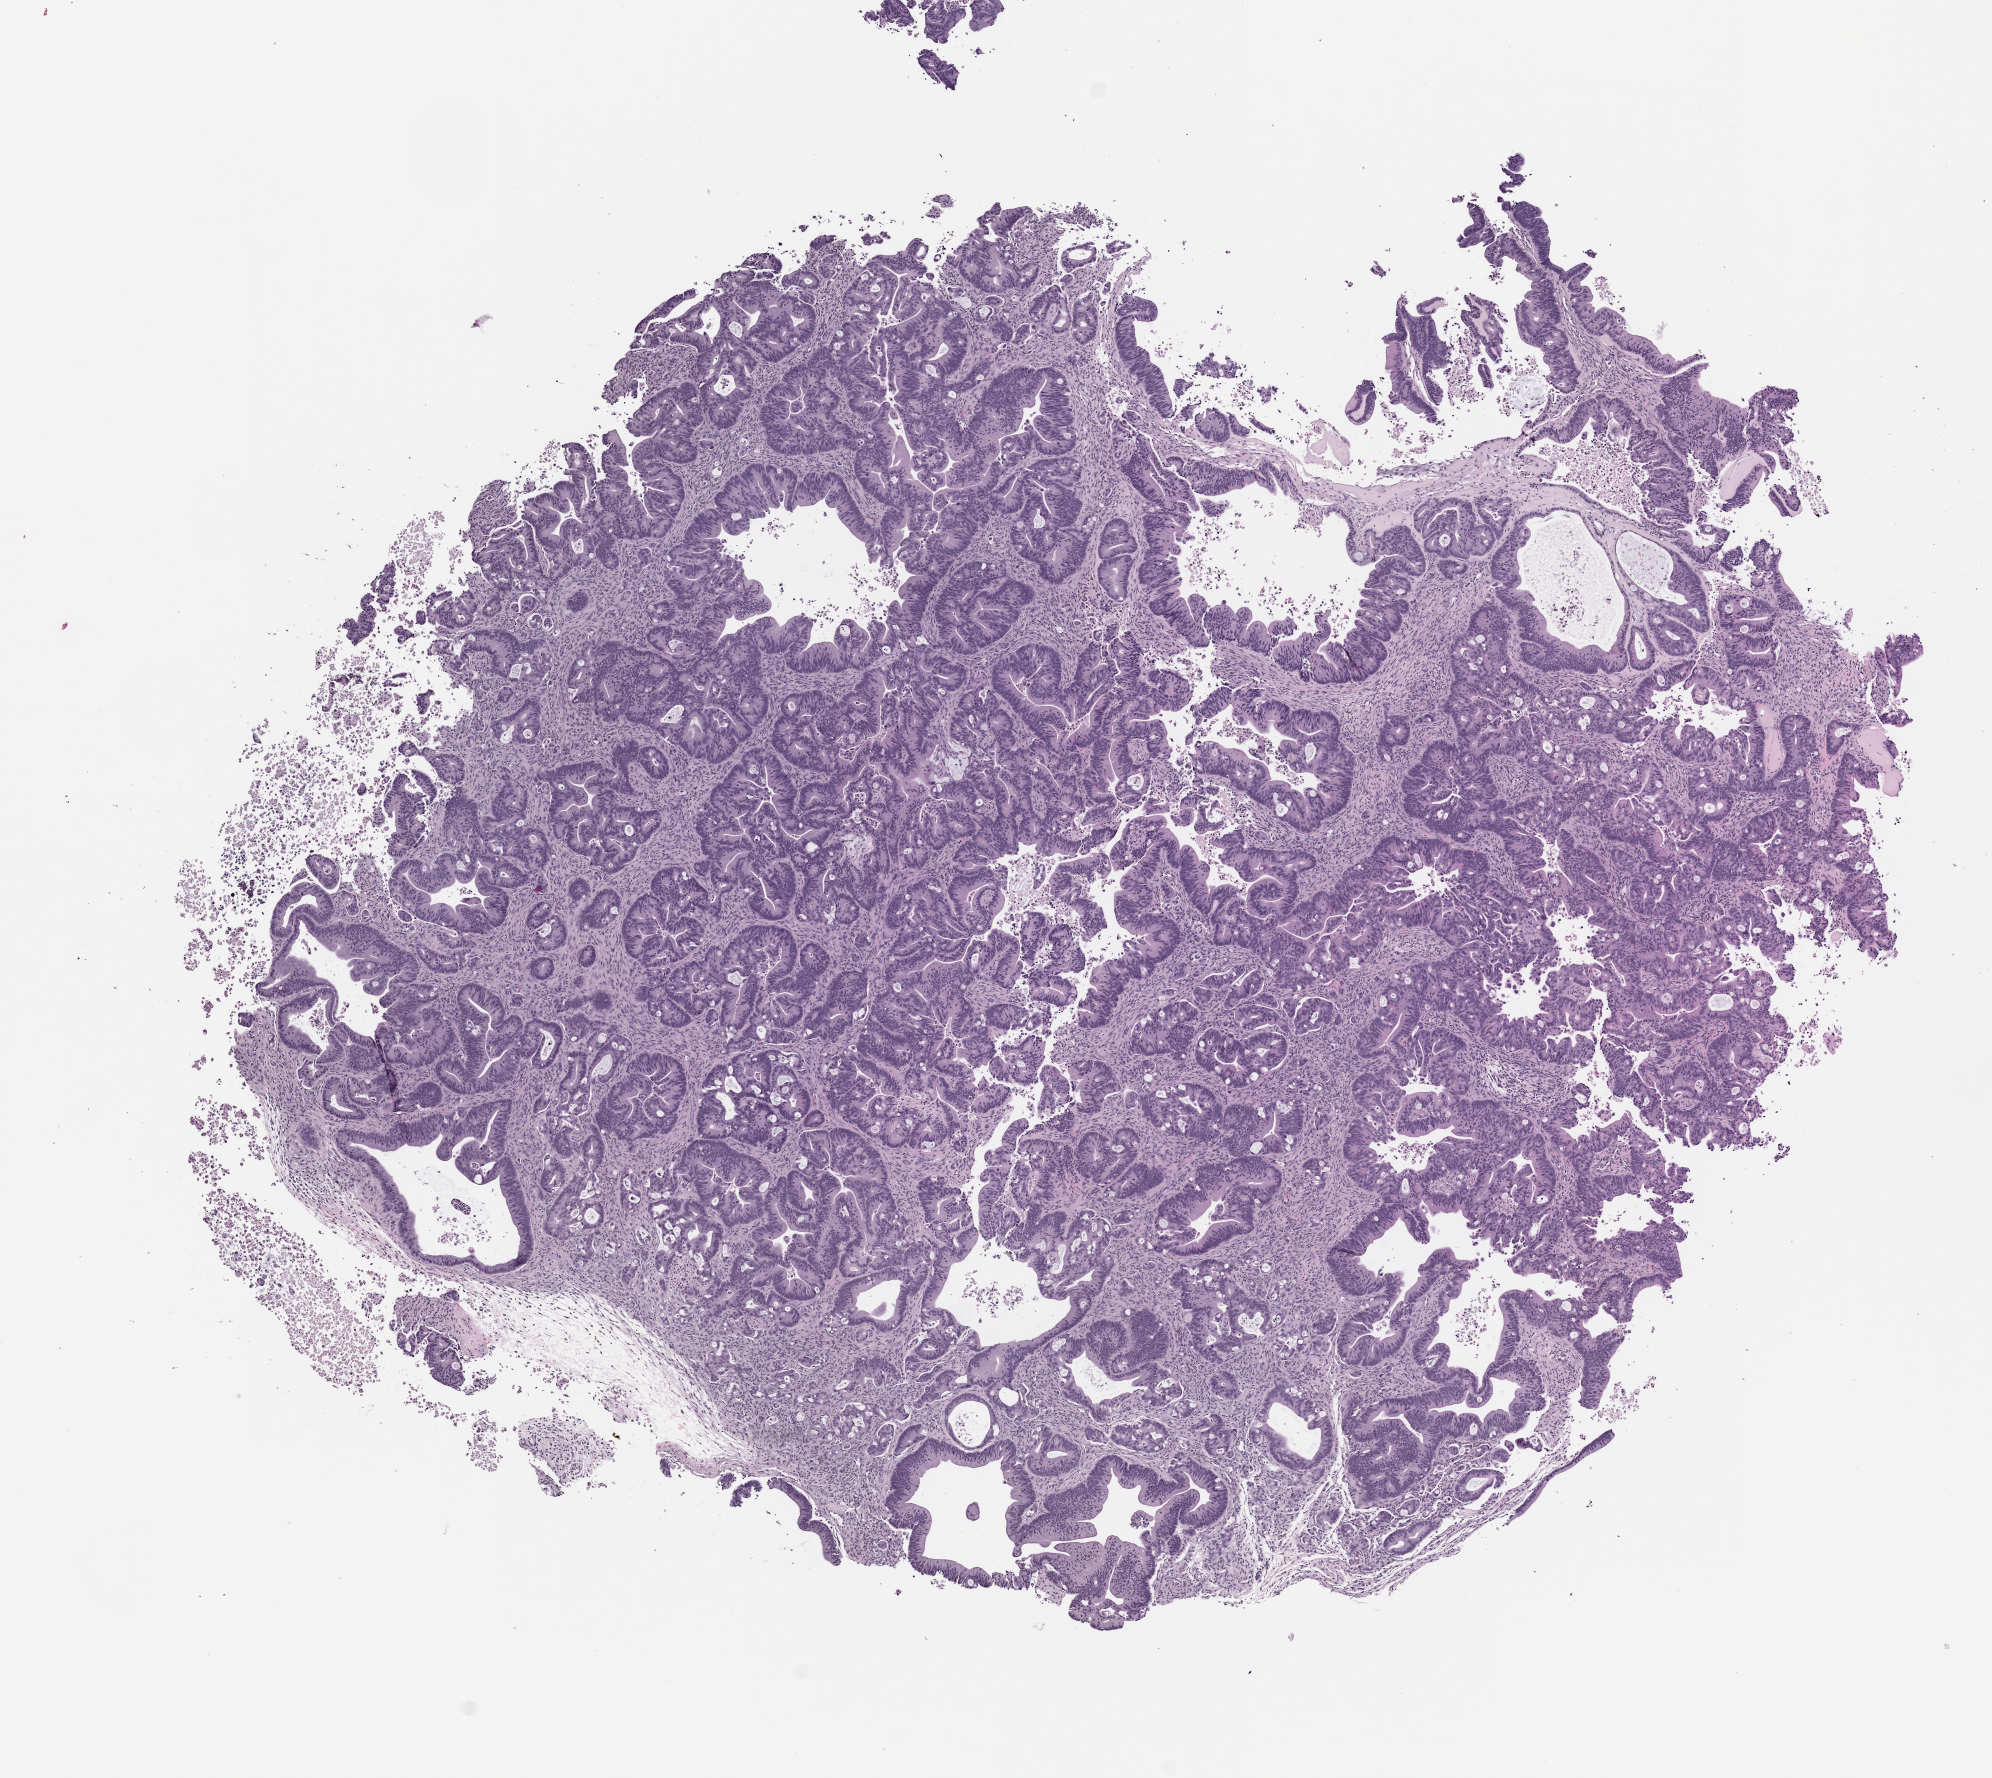
Hematoxylin and eosin (H&E) whole-slide image of a patient-derived xenograft (PDX) tumor grown in a mouse, passage 3 — low-resolution overview of the scanned area, about 8.0 x 7.2 mm. FFPE section. Tumor site category: rectum.
* originating patient diagnosis: Rectal Adenocarcinoma